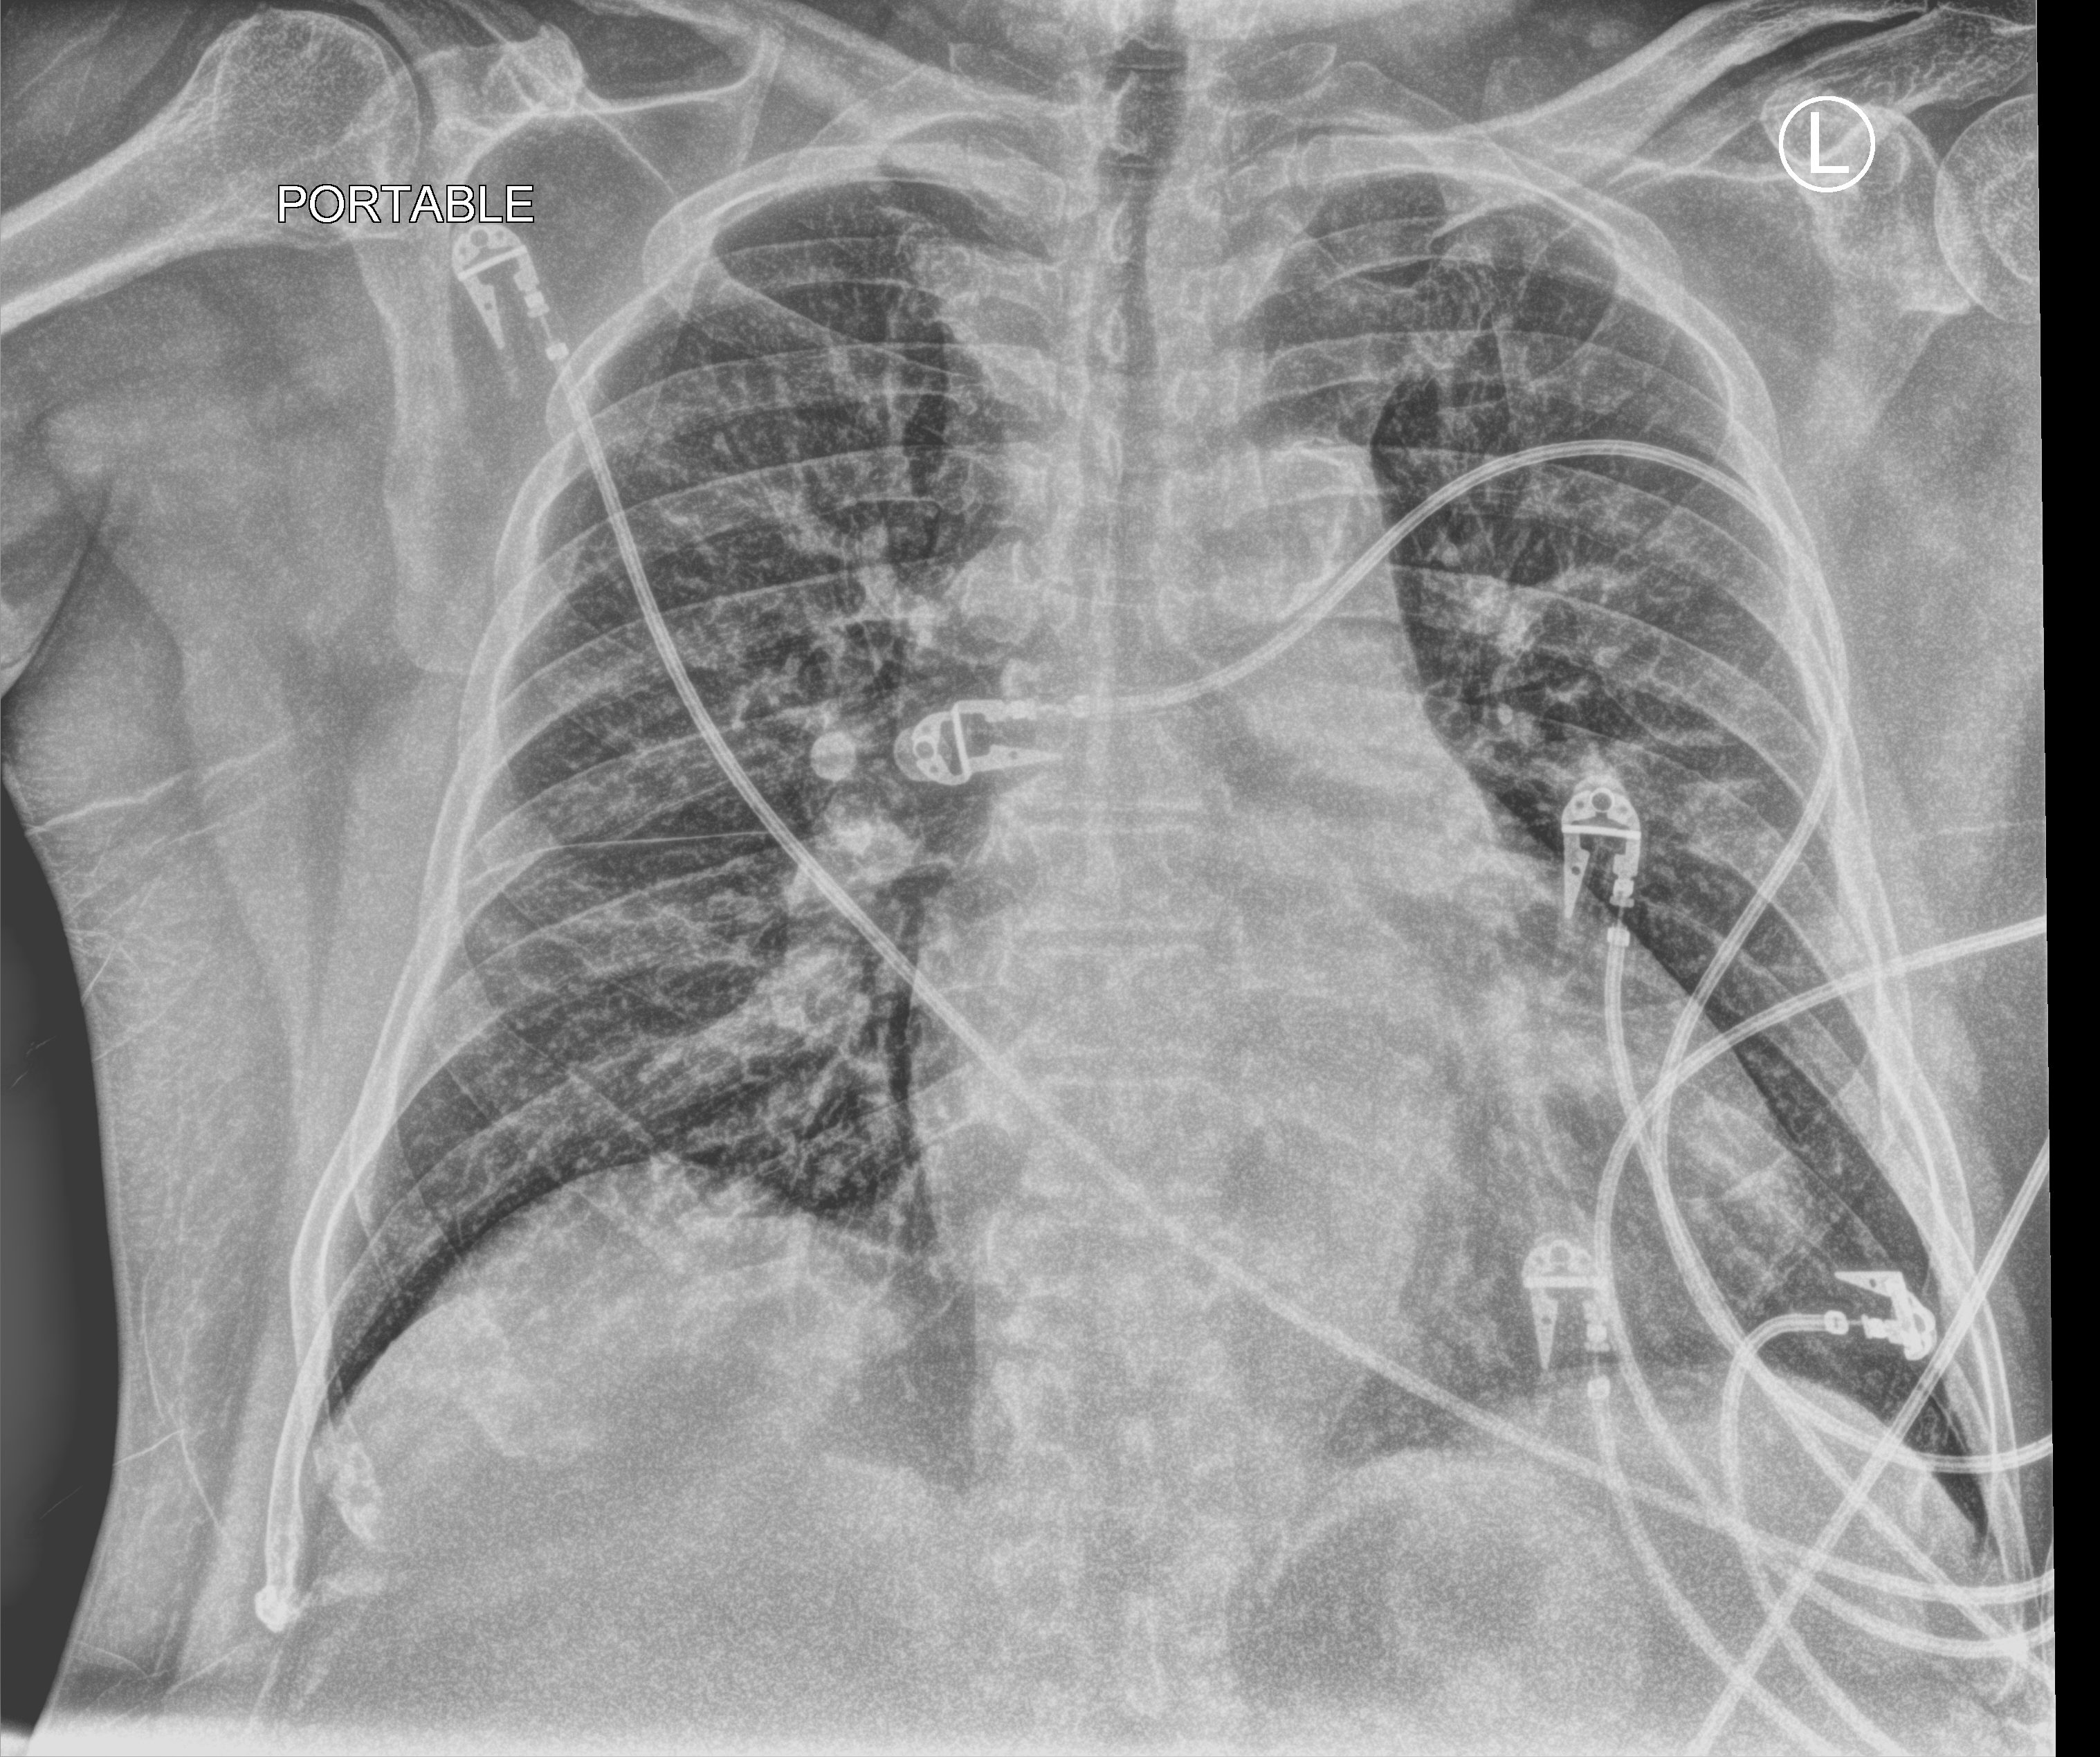
Chest X-ray (portable); anteroposterior (AP) projection. Patient hospitalised with COVID-19; male, aged 60–74 years.
Hospital-stay facts (about this admission, not read from this image; timing relative to this image not recorded): length of hospital stay: 10 days; mechanically ventilated during this hospital stay: no; admitted to intensive care during this hospital stay: yes.